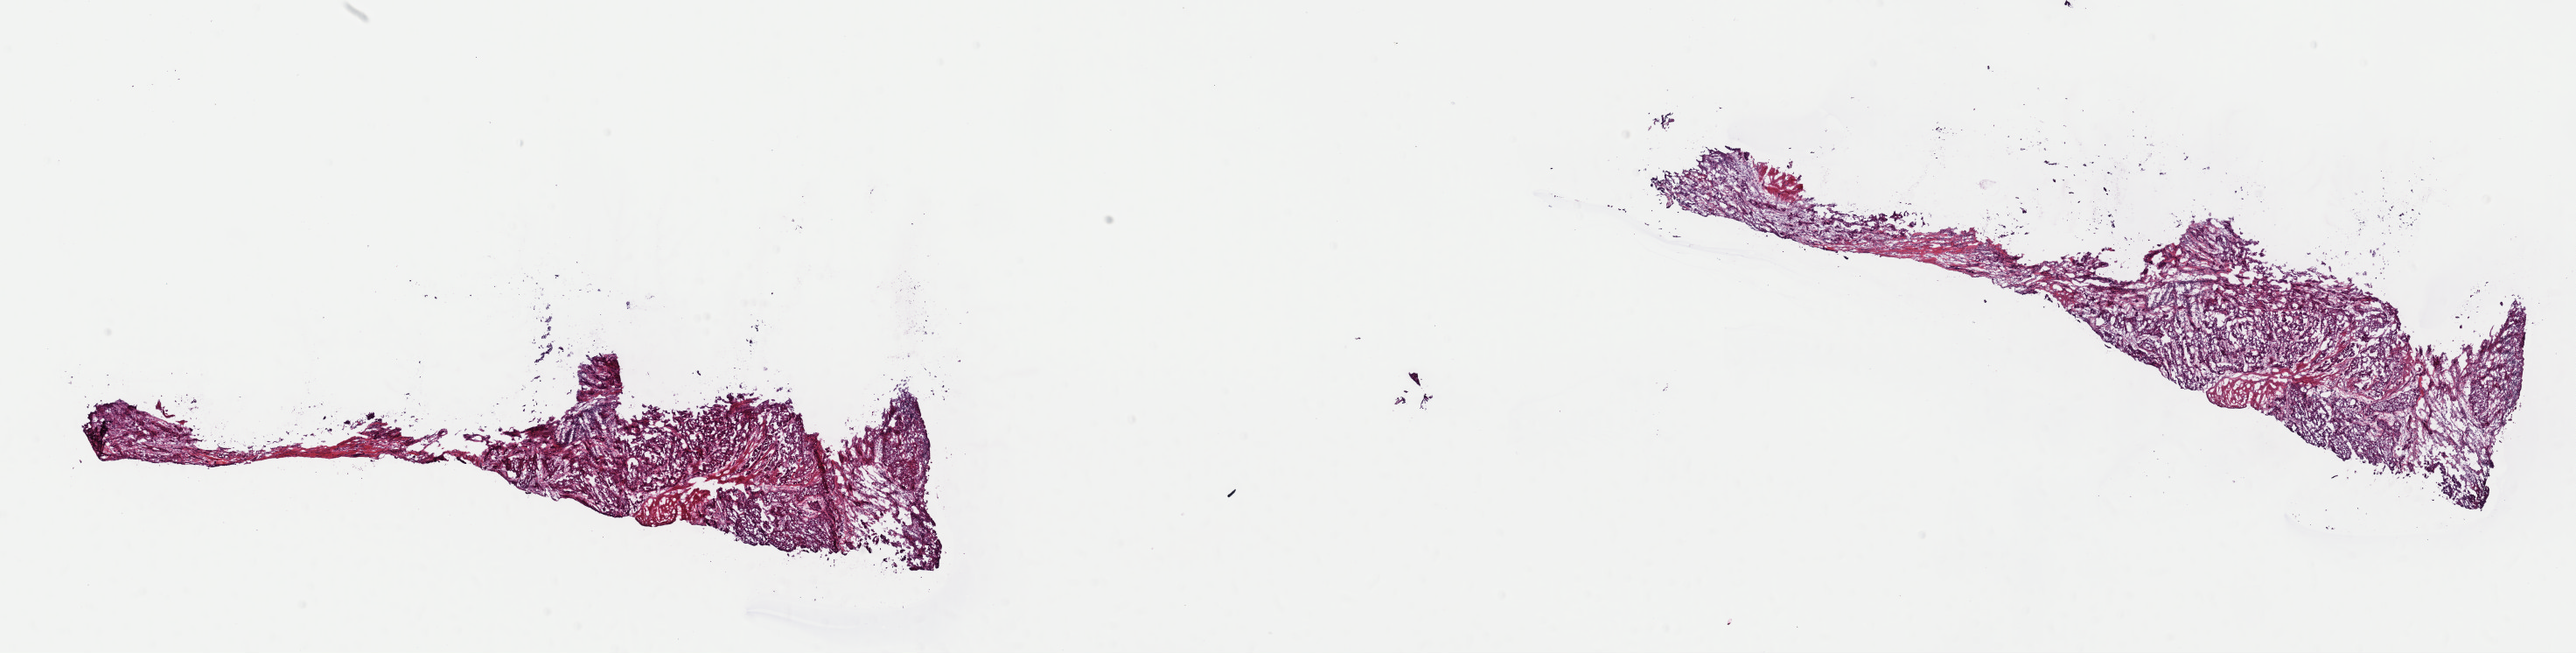
Whole-slide histology image, H&E-stained — low-resolution overview of the scanned area, about 23.3 x 5.9 mm, frozen section from the top of the tissue portion, primary tumour sample from the bladder. Patient: male, age at initial diagnosis 66 years. Histologic grade: high grade. Slide review estimates, as recorded: tumour cells 70%, tumour nuclei 70%, normal cells 0%, stromal cells 30%, necrosis 0%. Inflammatory infiltration, as recorded: lymphocyte infiltration 5%, monocyte infiltration 0%, neutrophil infiltration 0%.
* AJCC pathologic stage: IV (7th edition)
* diagnosis: Transitional cell carcinoma (trigone of bladder)